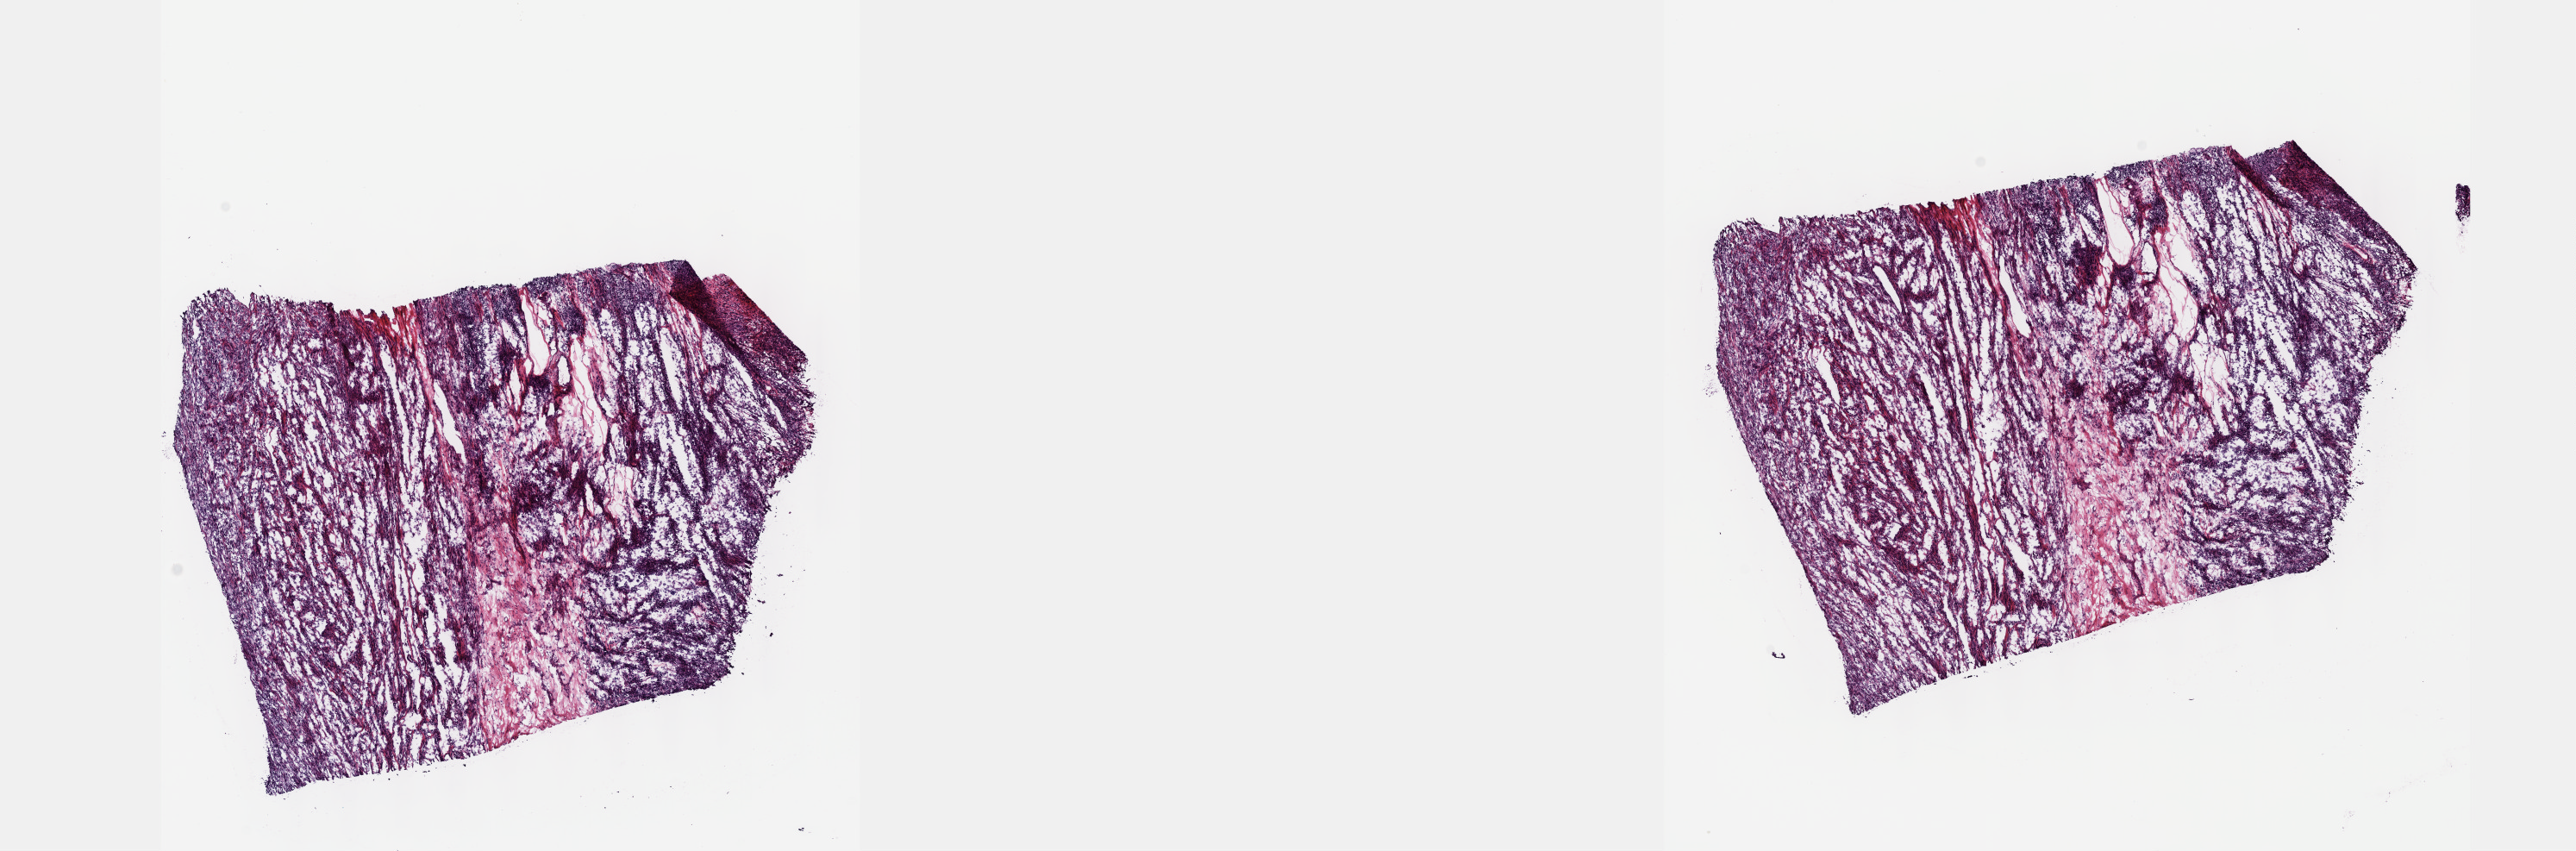
H&E-stained whole-slide image, a low-resolution overview of the entire scanned area, about 24.1 x 8.0 mm (acquisition: 40x scan), frozen section from the top of the tissue portion, primary tumour sample from the connective, subcutaneous and other soft tissues. Patient: male, age at initial diagnosis 58 years. Composition of this section per pathologist review: tumour cells 80%, tumour nuclei 80%, normal cells 0%, stromal cells 19%, necrosis 1%. Inflammatory infiltration, as recorded: lymphocyte infiltration 2%, monocyte infiltration 2%, neutrophil infiltration 1%.
- diagnosis: Malignant fibrous histiocytoma (connective, subcutaneous and other soft tissues of lower limb and hip)